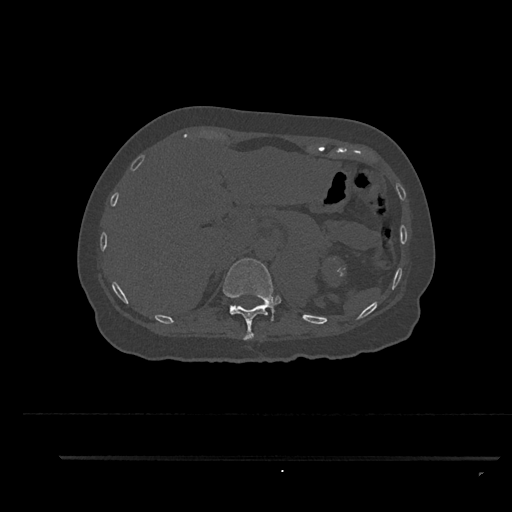
CT including the spine, one axial slice. Bone window (W 1800 / L 400 HU). 512 × 512 image matrix, field of view 408 × 408 mm. Patient: female, 44 years. Case-level facts recorded for this patient, not image findings: primary cancer: renal; vertebrae with lytic lesions (as recorded): L1.
Annotated regions visible in this slice (semi-automatically segmented with operator editing):
- T11 vertebra: bounding box [x1, y1, x2, y2] px = [223, 258, 275, 340]